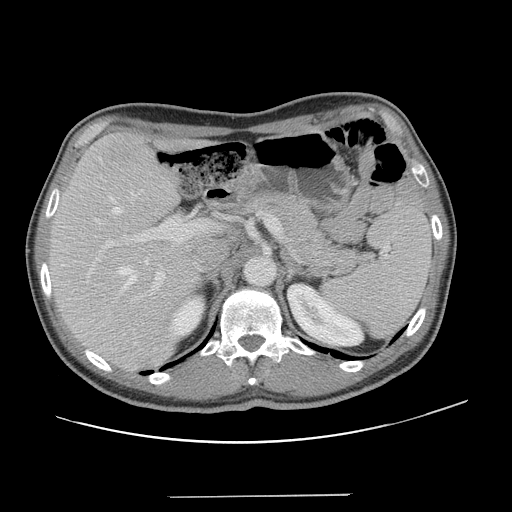
Contrast-enhanced abdominal CT, one axial slice. Position 87 of 131 along the scan axis. 120 kVp. Intravenous contrast given. Soft-tissue window (W 400 / L 40 HU). 512 × 512 image matrix. Male patient, age 60 years. Case-level facts recorded for this patient, not image findings: diagnosis: colorectal cancer liver metastases, imaged before liver resection; multiple liver metastases: no; largest metastasis: 2.5 cm; disease in both lobes: no.
Structures marked on this image (manually delineated by an expert):
- hepatic veins: bounding box <109,196,148,292> (left, top, right, bottom; pixels)
- liver: <49,132,199,370>
- planned liver remnant (the part of the liver to remain after resection): <49,132,200,355>
- portal vein (with intrahepatic branches): <99,219,220,288>